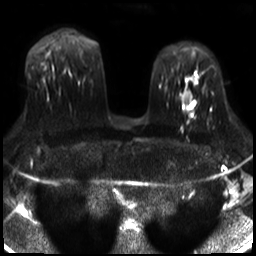
Breast MRI, one axial slice; slice 19 of 30 in the series (ordered by position); diffusion-weighted series; image 2 of 4 stored at this slice position (different b-values; order by instance number); 3 T; 4 mm slice thickness; 256 × 256 image matrix, field of view 320 × 320 mm. Female patient.
Outlined on this slice (expert manual segmentation):
- tumour on diffusion-weighted imaging: box from (x=183, y=92) to (x=190, y=96) px